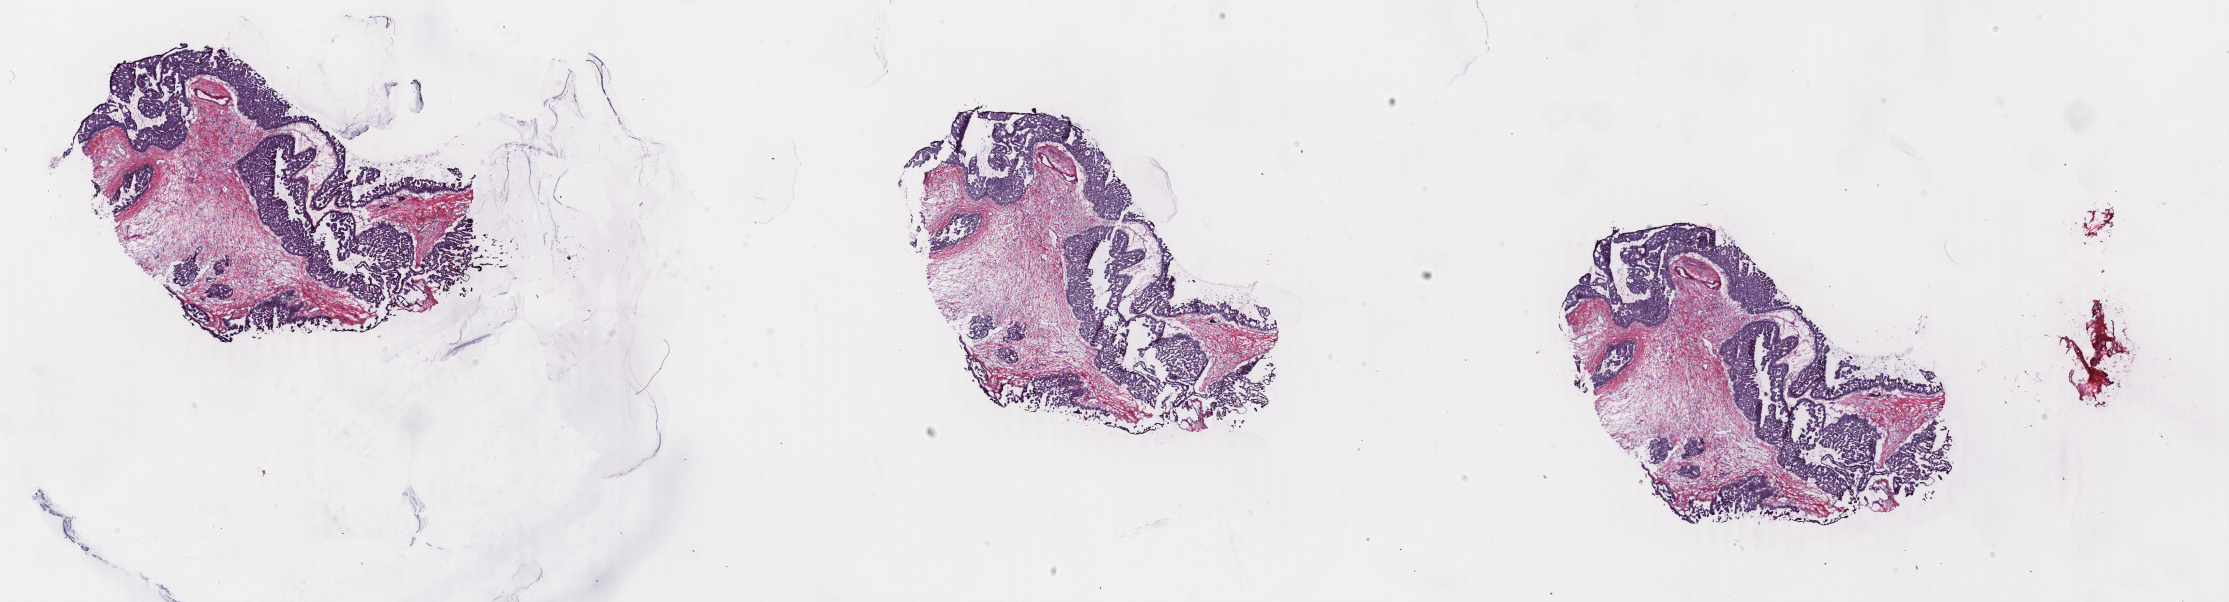
H&E-stained whole-slide image, a low-resolution overview of the entire scanned area, about 35.5 x 9.6 mm (from a 40x scan), frozen section from the top of the tissue portion, primary tumour sample from the breast. Female patient; age at initial diagnosis 63 years. Slide review estimates, as recorded: tumour cells 85%, tumour nuclei 85%, normal cells 0%, stromal cells 15%, necrosis 0%. Infiltration values recorded for this section: lymphocyte infiltration 1%, monocyte infiltration 0%, neutrophil infiltration 0%.
Pathologic diagnosis: Infiltrating duct carcinoma, NOS. AJCC pathologic stage: IA.